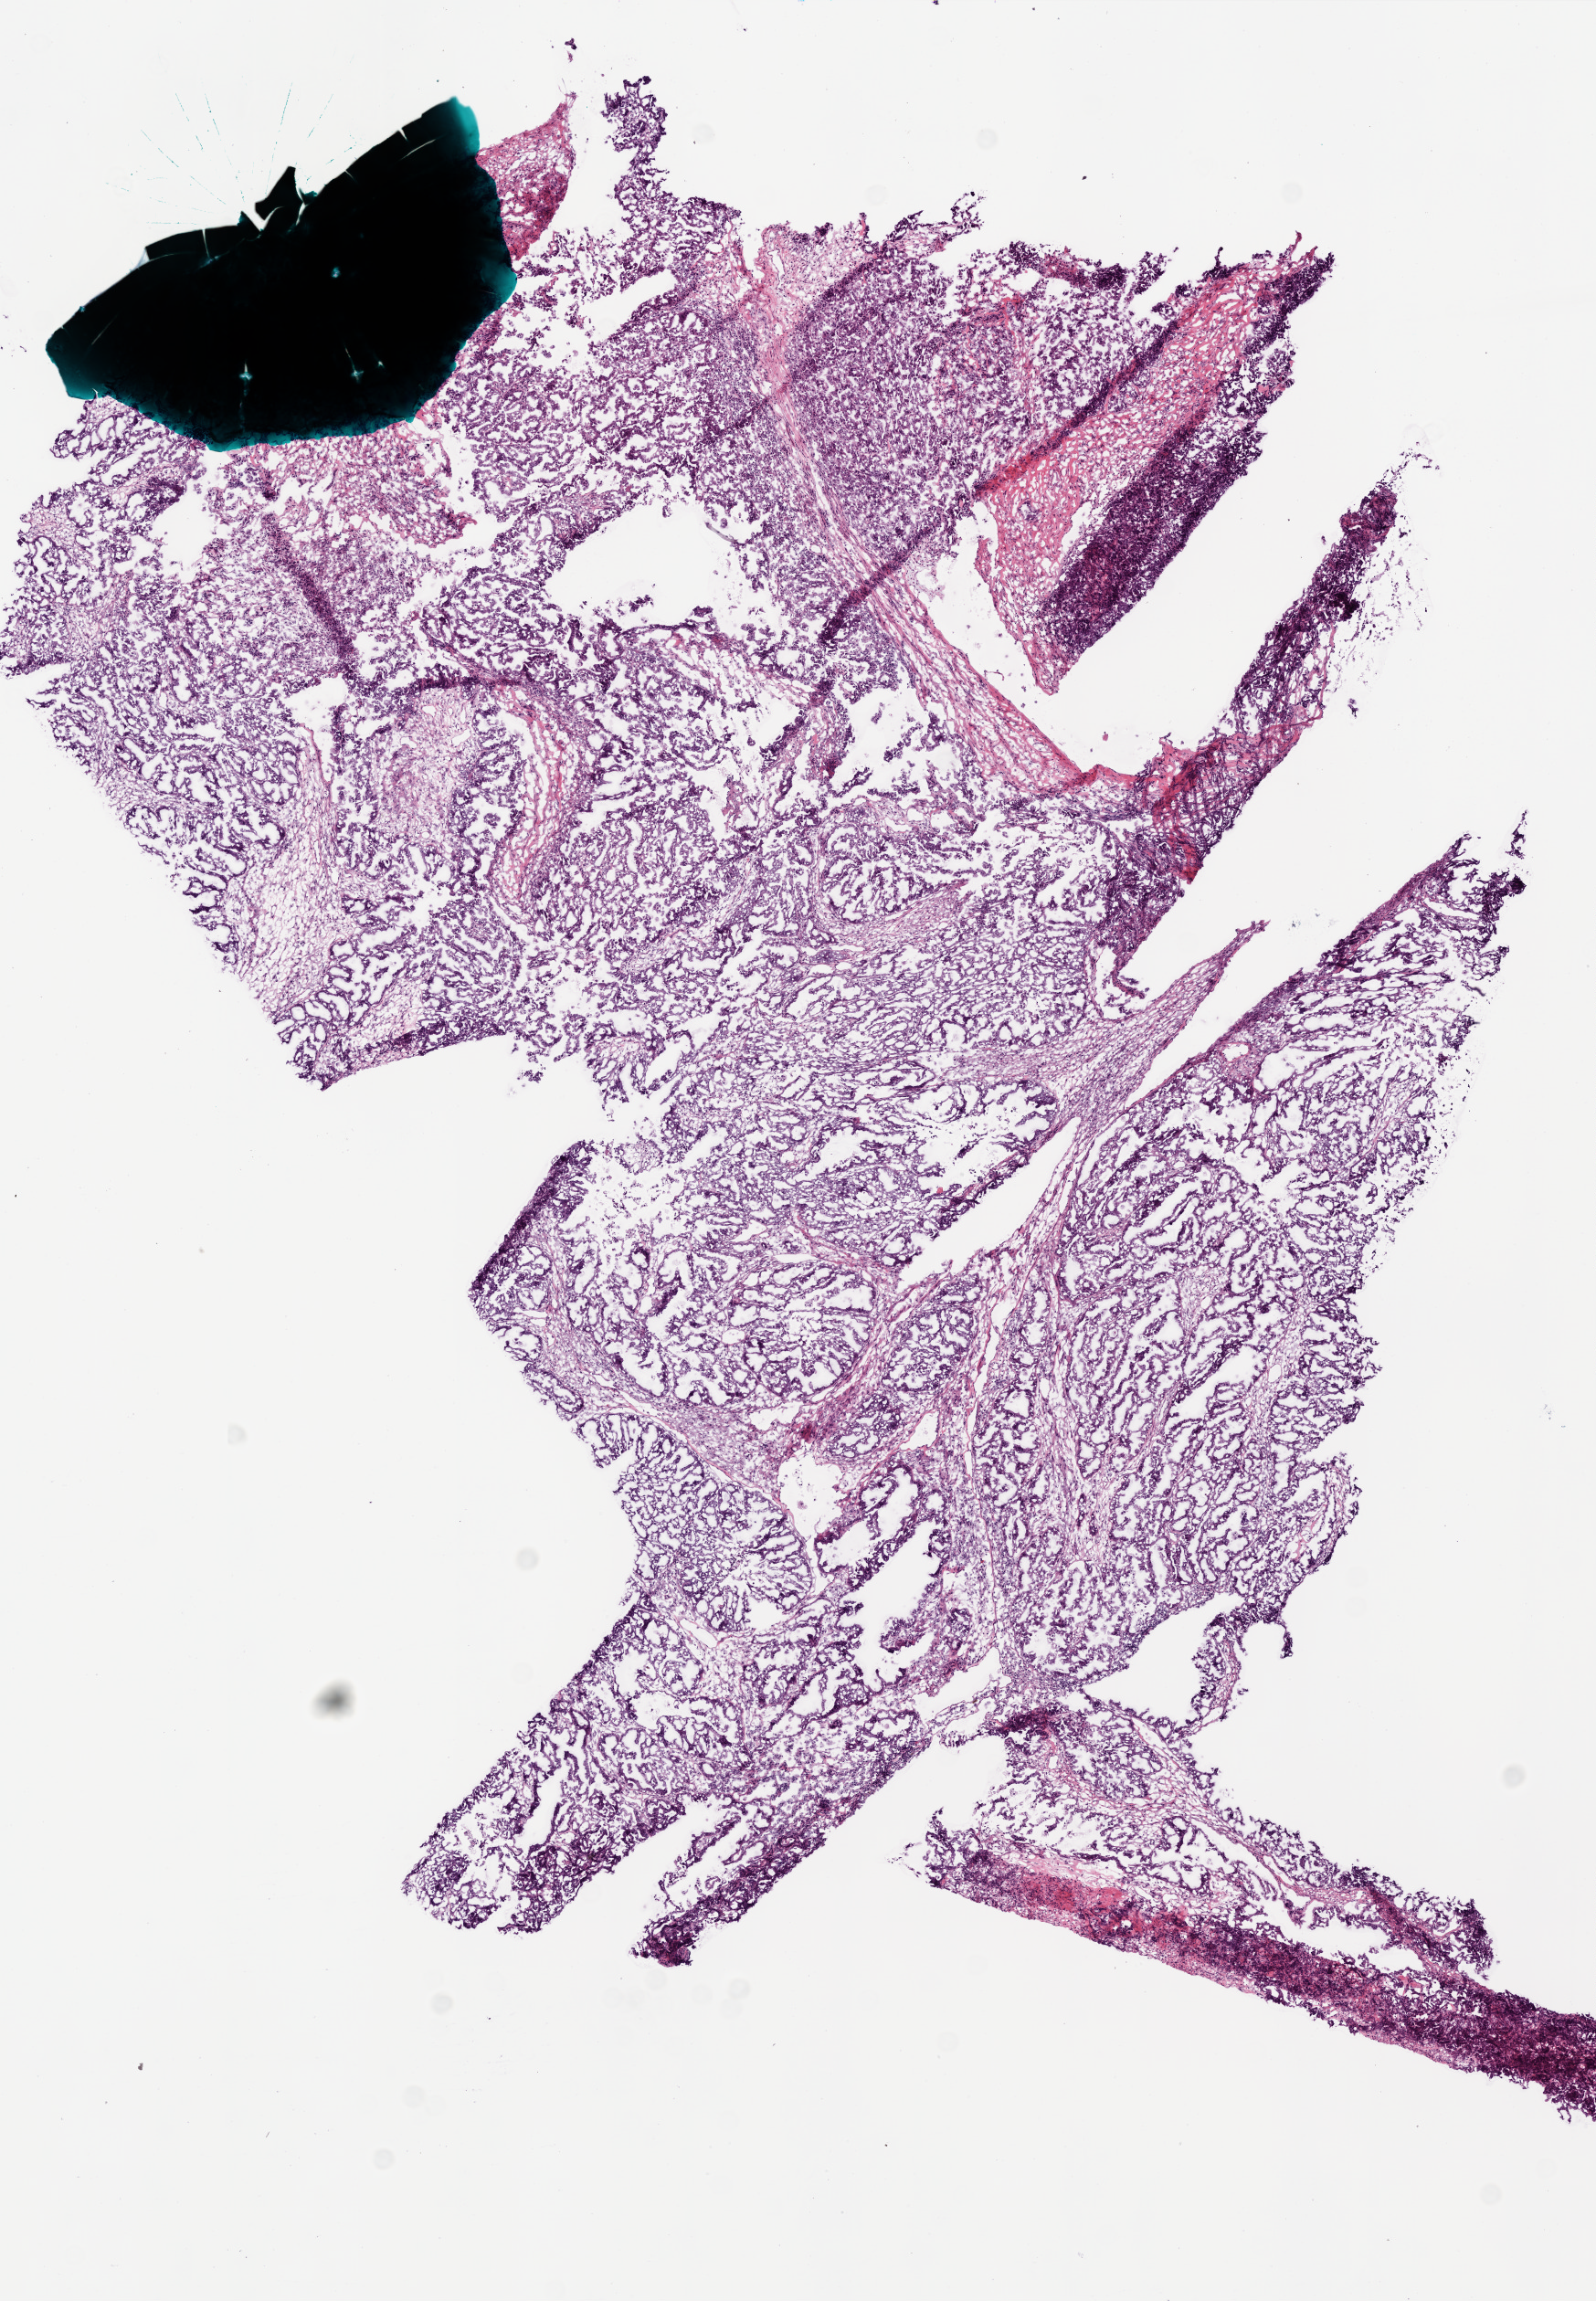
H&E whole-slide image, low-resolution overview of the scanned area, about 7.0 x 10.1 mm, frozen section from the bottom of the tissue portion, sample: primary tumour, ovary. Female patient; age at initial diagnosis 64 years. Histologic grade: G3 (poorly differentiated). Pathologist review of this section (percent, as recorded): tumour cells 0%, tumour nuclei 95%, normal cells 0%, stromal cells 0%, necrosis 1%.
- FIGO stage: IIIC
- laterality: left
- pathologic diagnosis: Serous cystadenocarcinoma, NOS